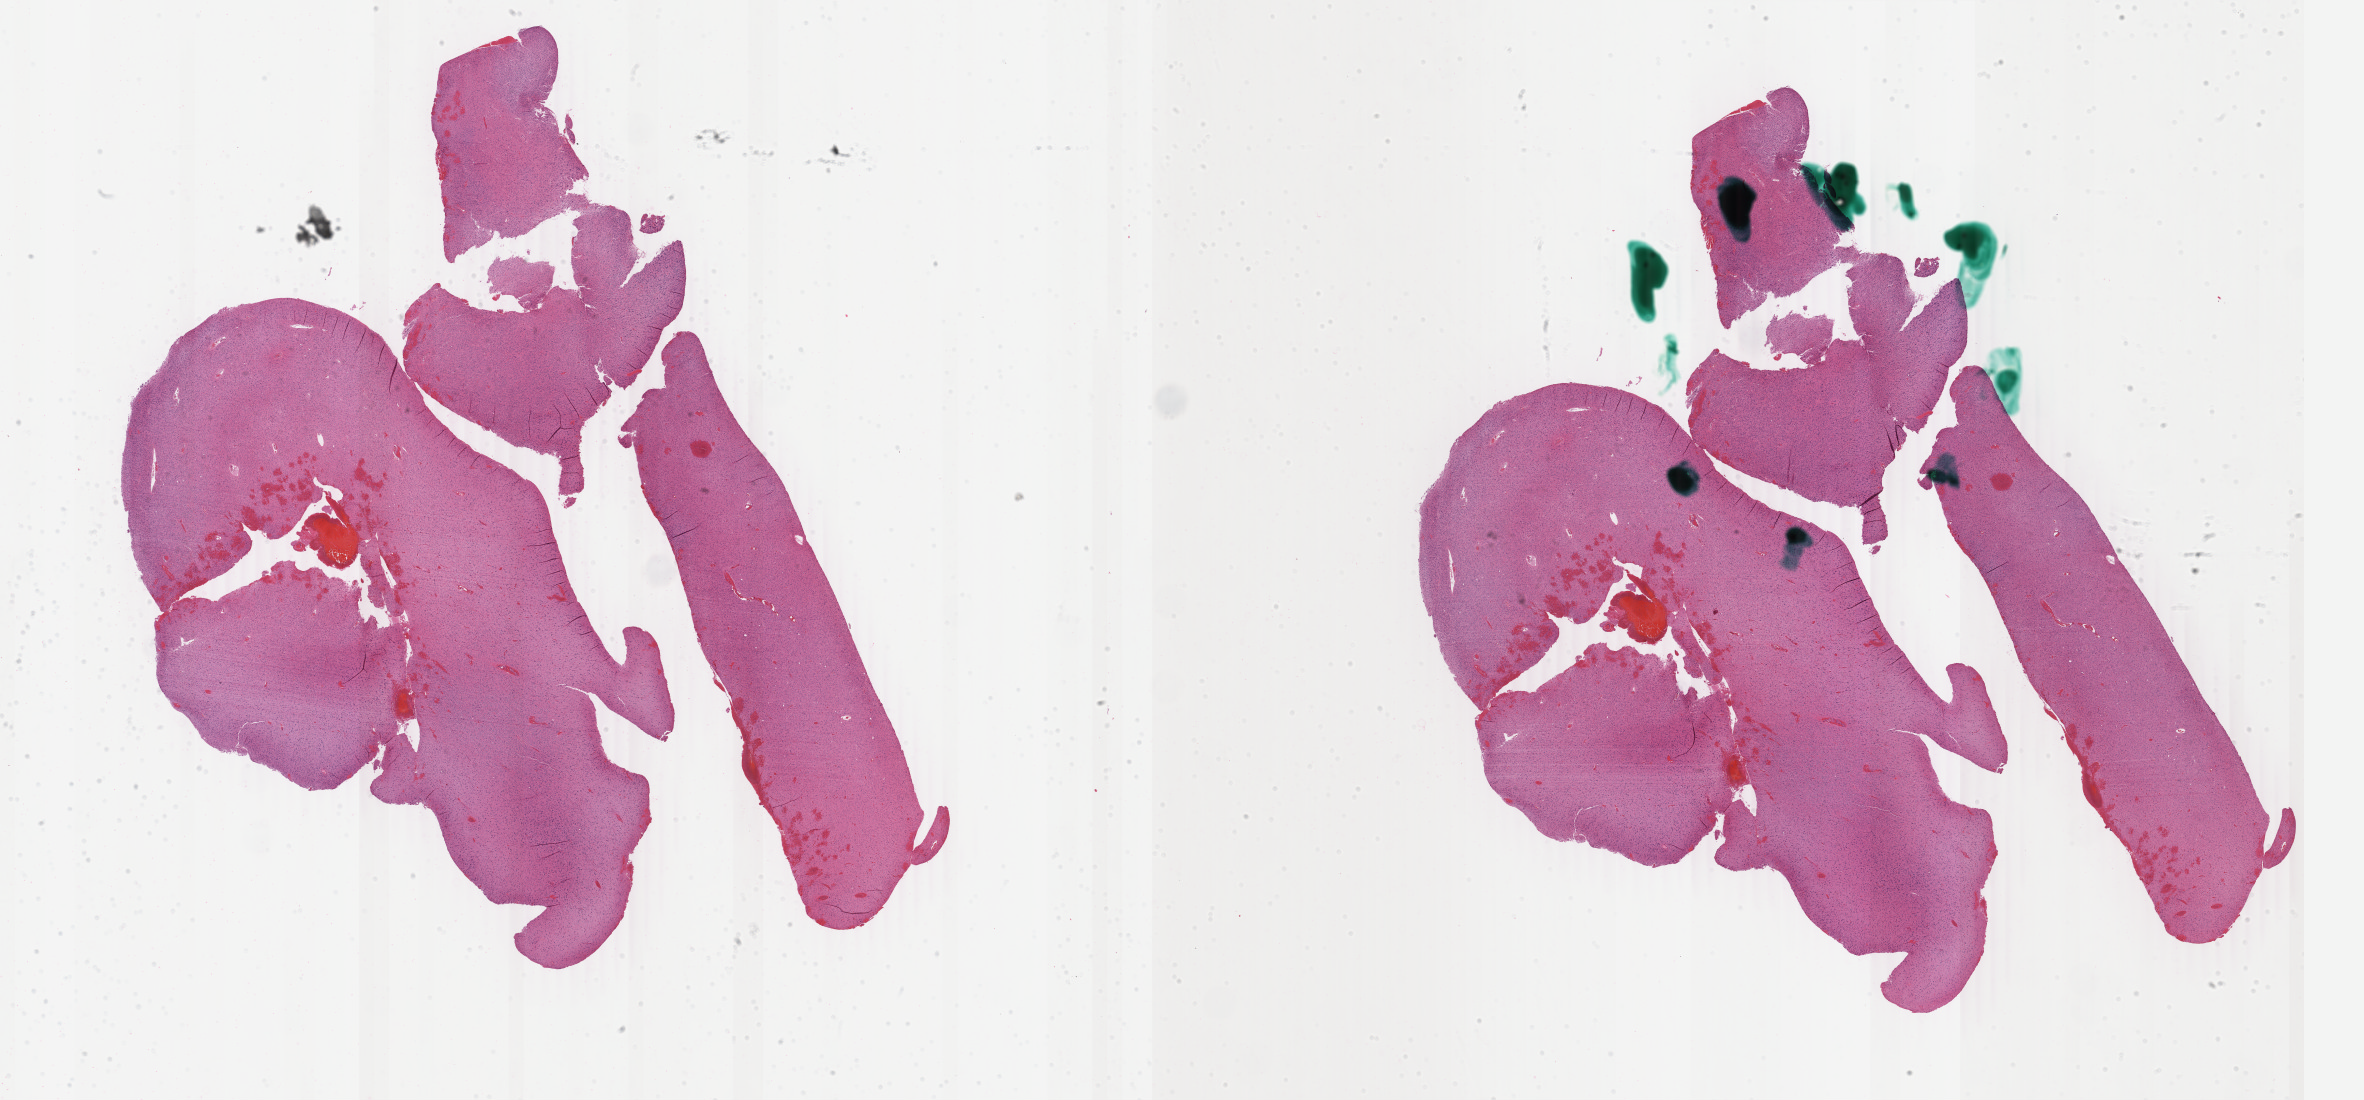
Digitized Hematoxylin and eosin (H&E) stained tissue section (whole slide) — a low-resolution overview of the entire scanned area, about 37.6 x 17.5 mm. Formalin-fixed paraffin-embedded (FFPE) diagnostic section. Brain, primary tumour sample. Patient: male, age at initial diagnosis 50 years. Histologic grade: G2 (moderately differentiated).
Histologic diagnosis: Oligodendroglioma, NOS (cerebrum).